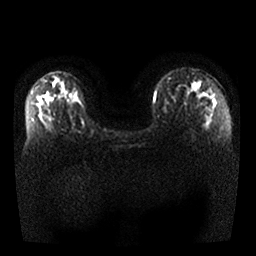
Breast MRI, one axial slice; position 17 of 25 along the scan axis; diffusion-weighted series; image 2 of 4 stored at this slice position (different b-values; order by instance number); 1.5 T; 4 mm slice thickness; 256 × 256 image matrix. Female patient.
Structures marked on this image (manually delineated by an expert):
- tumour on diffusion-weighted imaging: bounding box (x1, y1, x2, y2) in pixels: (191, 81, 217, 108)